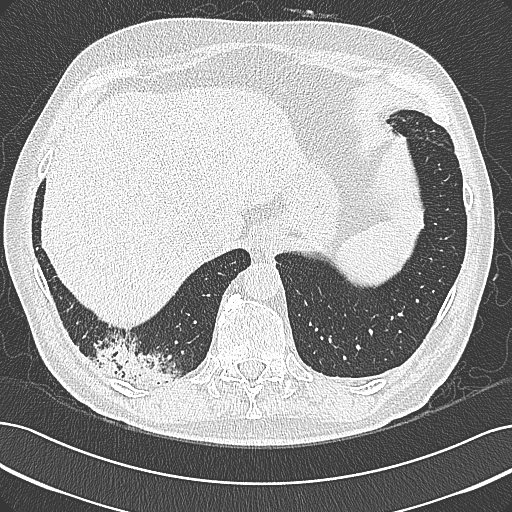
Chest CT (low-dose screening protocol), one axial image, first (baseline) screen, lung window (W 1500 / L -600 HU), 1 mm slice thickness, slice 248 of 355 in the series, 512 × 512 image matrix, field of view 362 × 362 mm. Male, age 68 years at enrolment. Former smoker at enrolment.
- Expert-annotated lung lesion, bounding box [x1, y1, x2, y2] px = [95, 338, 191, 399].
- No non-calcified nodule or mass ≥4 mm was recorded by the screening reader at this exam.